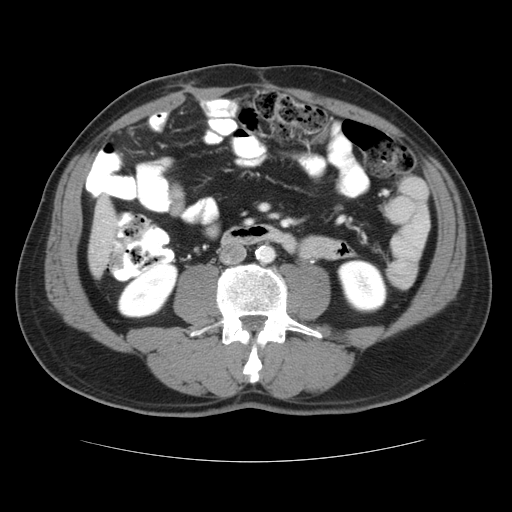
Contrast-enhanced abdominal CT, one axial slice; position 6 of 37 along the scan axis; reconstruction kernel STANDARD; soft-tissue window (W 400 / L 40 HU); 5 mm slice thickness; 512 × 512 image matrix, field of view 374 × 374 mm. Male patient, age 66 years. From the clinical record (not read from this slice): diagnosis: colorectal cancer liver metastases, imaged before liver resection; multiple liver metastases: yes; largest metastasis: 1.6 cm; disease in both lobes: yes.
Structures marked on this image (expert manual segmentation):
- liver: bounding box <89,195,119,276> (left, top, right, bottom; pixels)
- planned liver remnant (the part of the liver to remain after resection): <89,195,119,276>